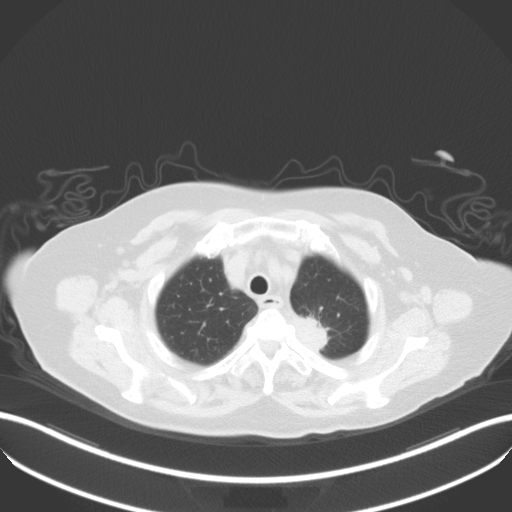
Chest CT, one axial slice. Slice 41 of 50 in the series (ordered by position). Reconstruction kernel B31f. 100 kVp. Lung window (W 1500 / L -600 HU). 512 × 512 image matrix, field of view 400 × 400 mm. Patient: female, 81 years. From the clinical record (not read from this slice): clinical TNM (as recorded): T2a N0 M0.
Annotated regions visible in this slice (bounding box drawn by a radiologist):
- lung tumour (recorded histology: adenocarcinoma): bounding box [x1, y1, x2, y2] px = [292, 309, 337, 358]